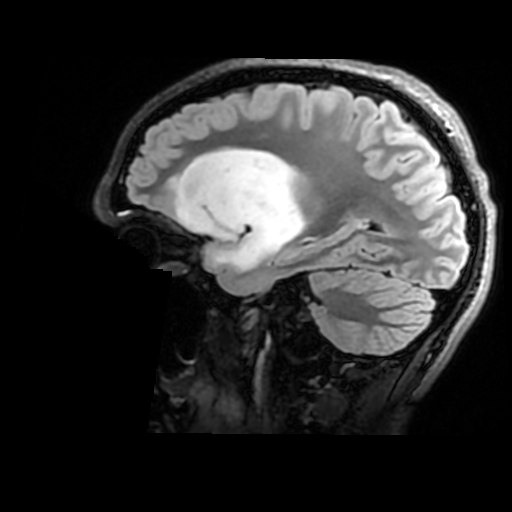
Brain MRI from a brain-tumour surgery series, one sagittal slice; slice 115 of 176 in the series (ordered by position); T2 FLAIR; 512 × 512 image matrix, field of view 240 × 240 mm. Case-level facts recorded for this patient, not image findings: histopathology: Astrocytoma; WHO grade: 2; IDH mutation: yes.
Outlined on this slice (outlined manually by an expert reader):
- tumour: box from (x=178, y=147) to (x=305, y=274) px